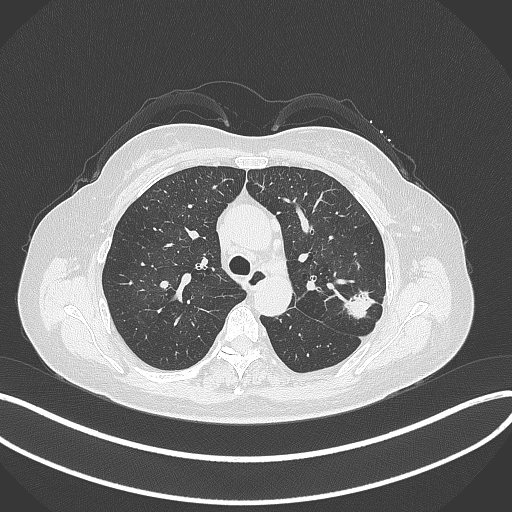
Chest CT, one axial slice; position 225 of 319 along the scan axis; lung window (W 1500 / L -600 HU); 1 mm slice thickness; 512 × 512 image matrix, field of view 400 × 400 mm. Patient: female, 60 years. Case-level facts recorded for this patient, not image findings: clinical TNM (as recorded): T1c N0 M0.
Structures marked on this image (bounding box drawn by a radiologist):
- lung tumour (recorded histology: adenocarcinoma): box from (x=337, y=281) to (x=376, y=324) px